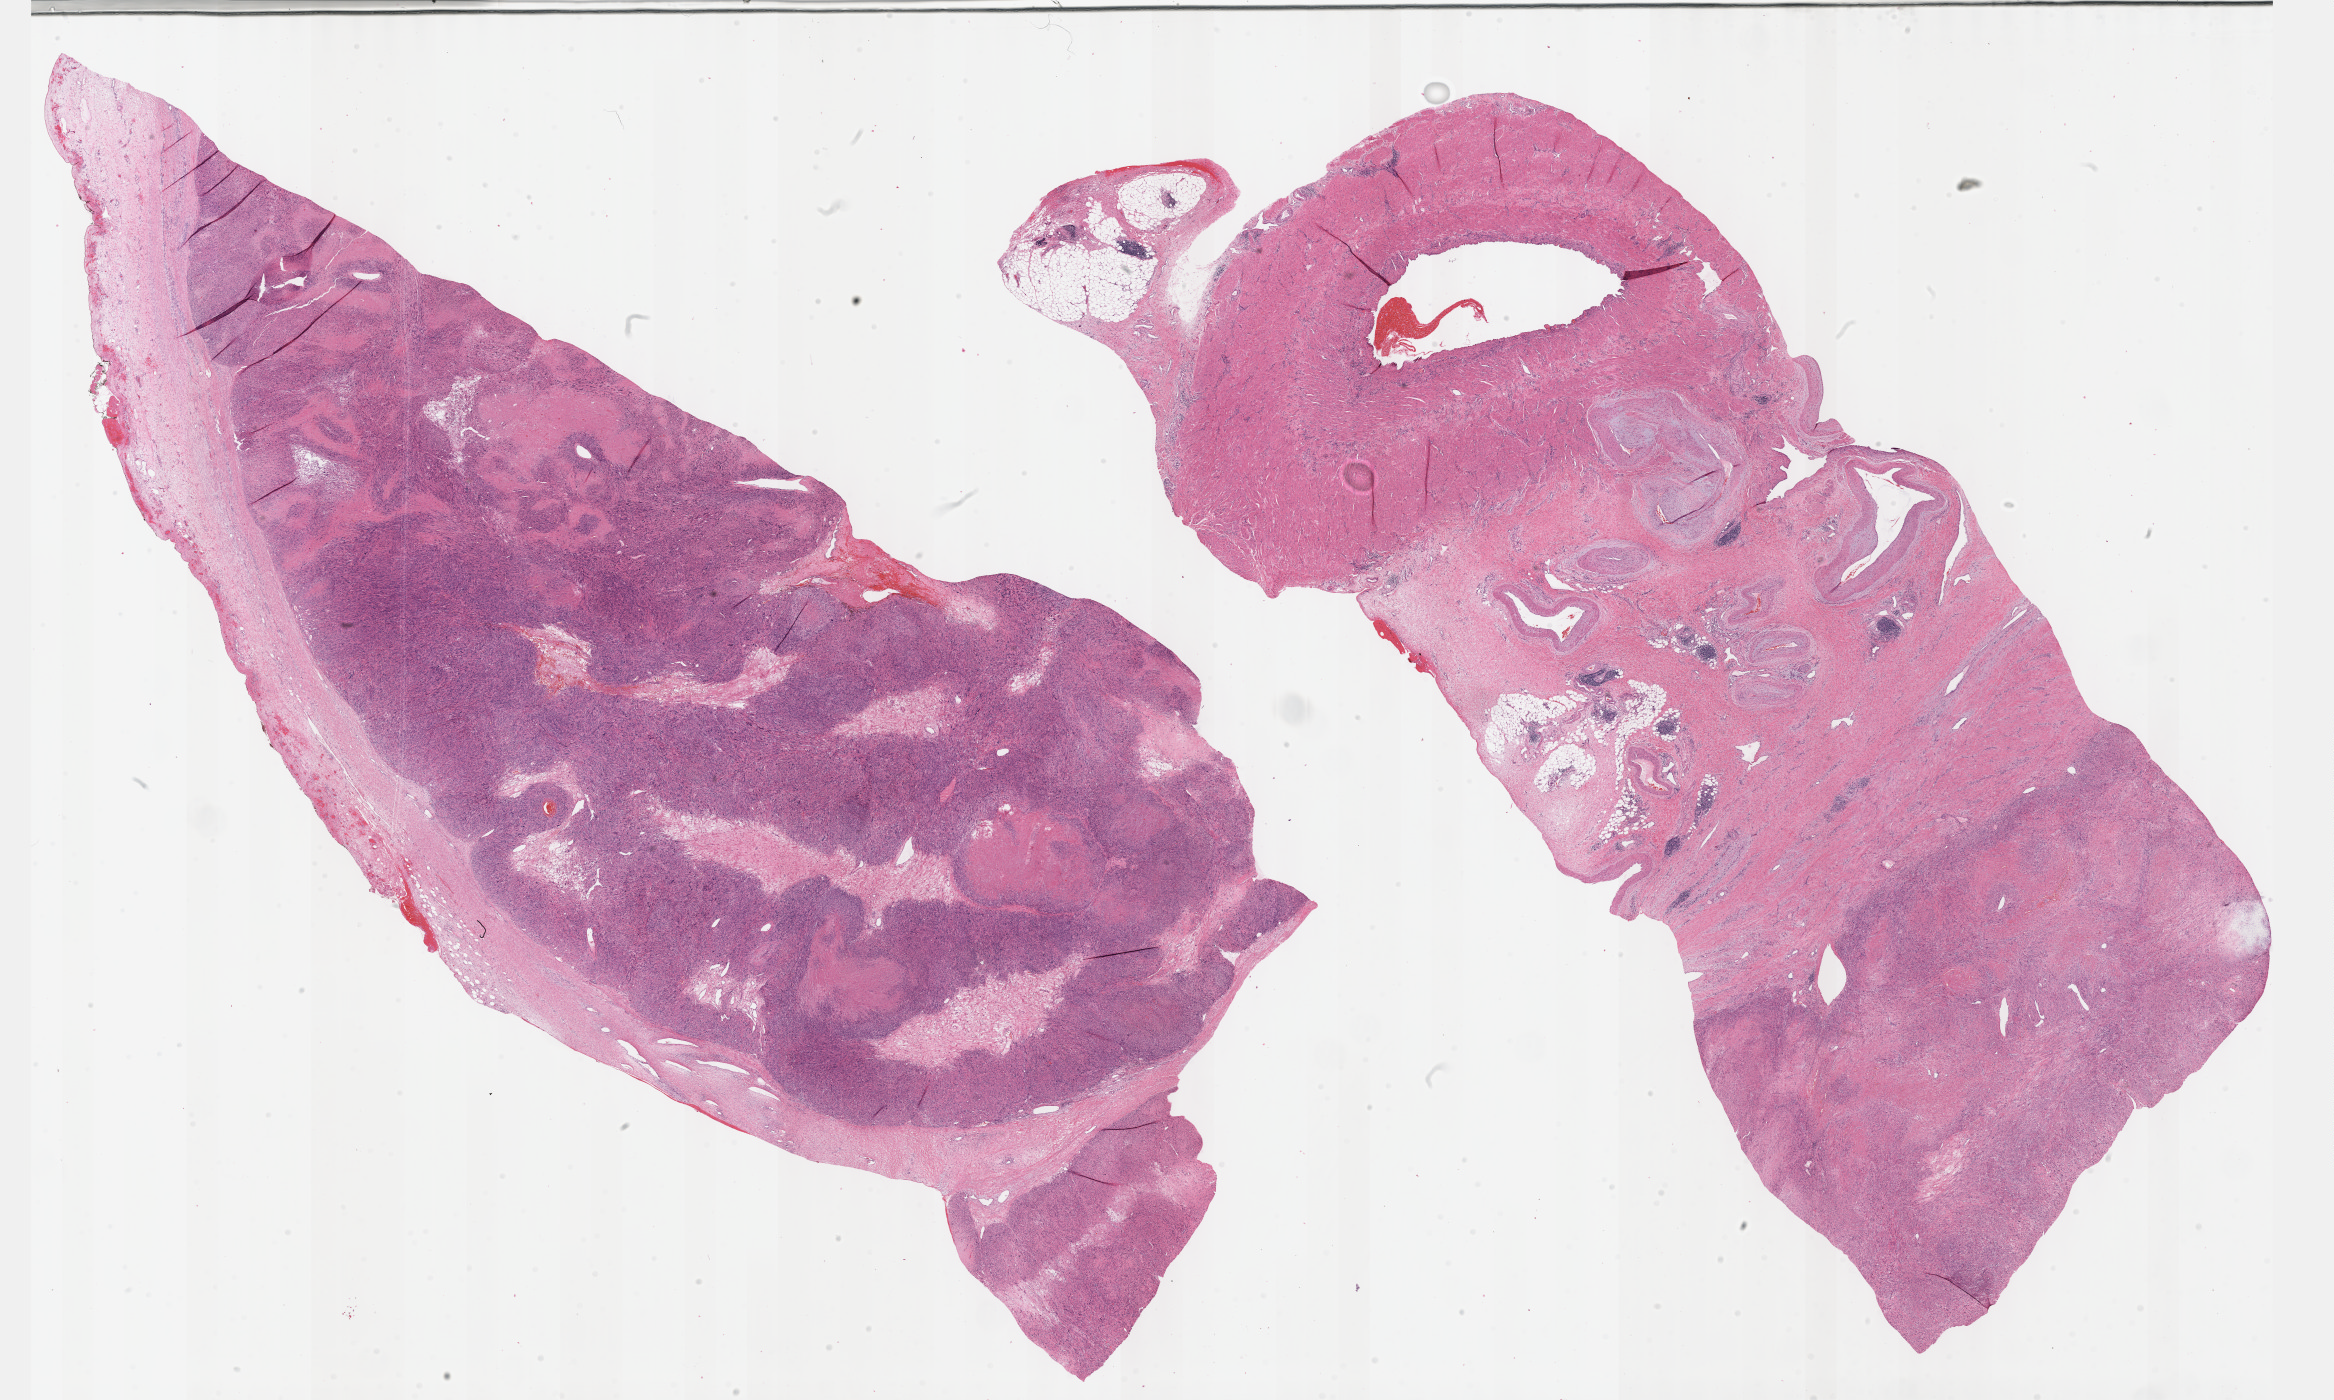
Whole-slide histology image, H&E — whole scanned area (about 37.7 x 22.6 mm, slide scanned at 40x) shown as a low-resolution overview. Formalin-fixed paraffin-embedded (FFPE) diagnostic section. Sample: primary tumour, retroperitoneum and peritoneum. Female patient; age at initial diagnosis 63 years.
Histologic diagnosis: Leiomyosarcoma, NOS (retroperitoneum).